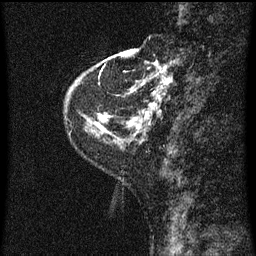
Breast MRI (dynamic contrast-enhanced), one sagittal slice. Slice 12 of 60 in the series (ordered by position). Dynamic contrast-enhanced series, image 2 of 3 at this slice position (ordered by acquisition). 1.5 T. TE 4.2 ms, TR 8 ms. 2 mm slice thickness. 256 × 256 image matrix, field of view 180 × 180 mm. Female patient, age 48 years.
Outlined on this slice (semi-automatic segmentation, software-assisted and operator-edited):
- analysis volume of interest (the breast-tissue region the enhancement analysis was run in; not a lesion): box from (x=128, y=54) to (x=173, y=125) px
- tumour enhancement mask (voxels above the 70 % enhancement threshold inside the analysis volume of interest): (x=128, y=62)–(x=173, y=125)